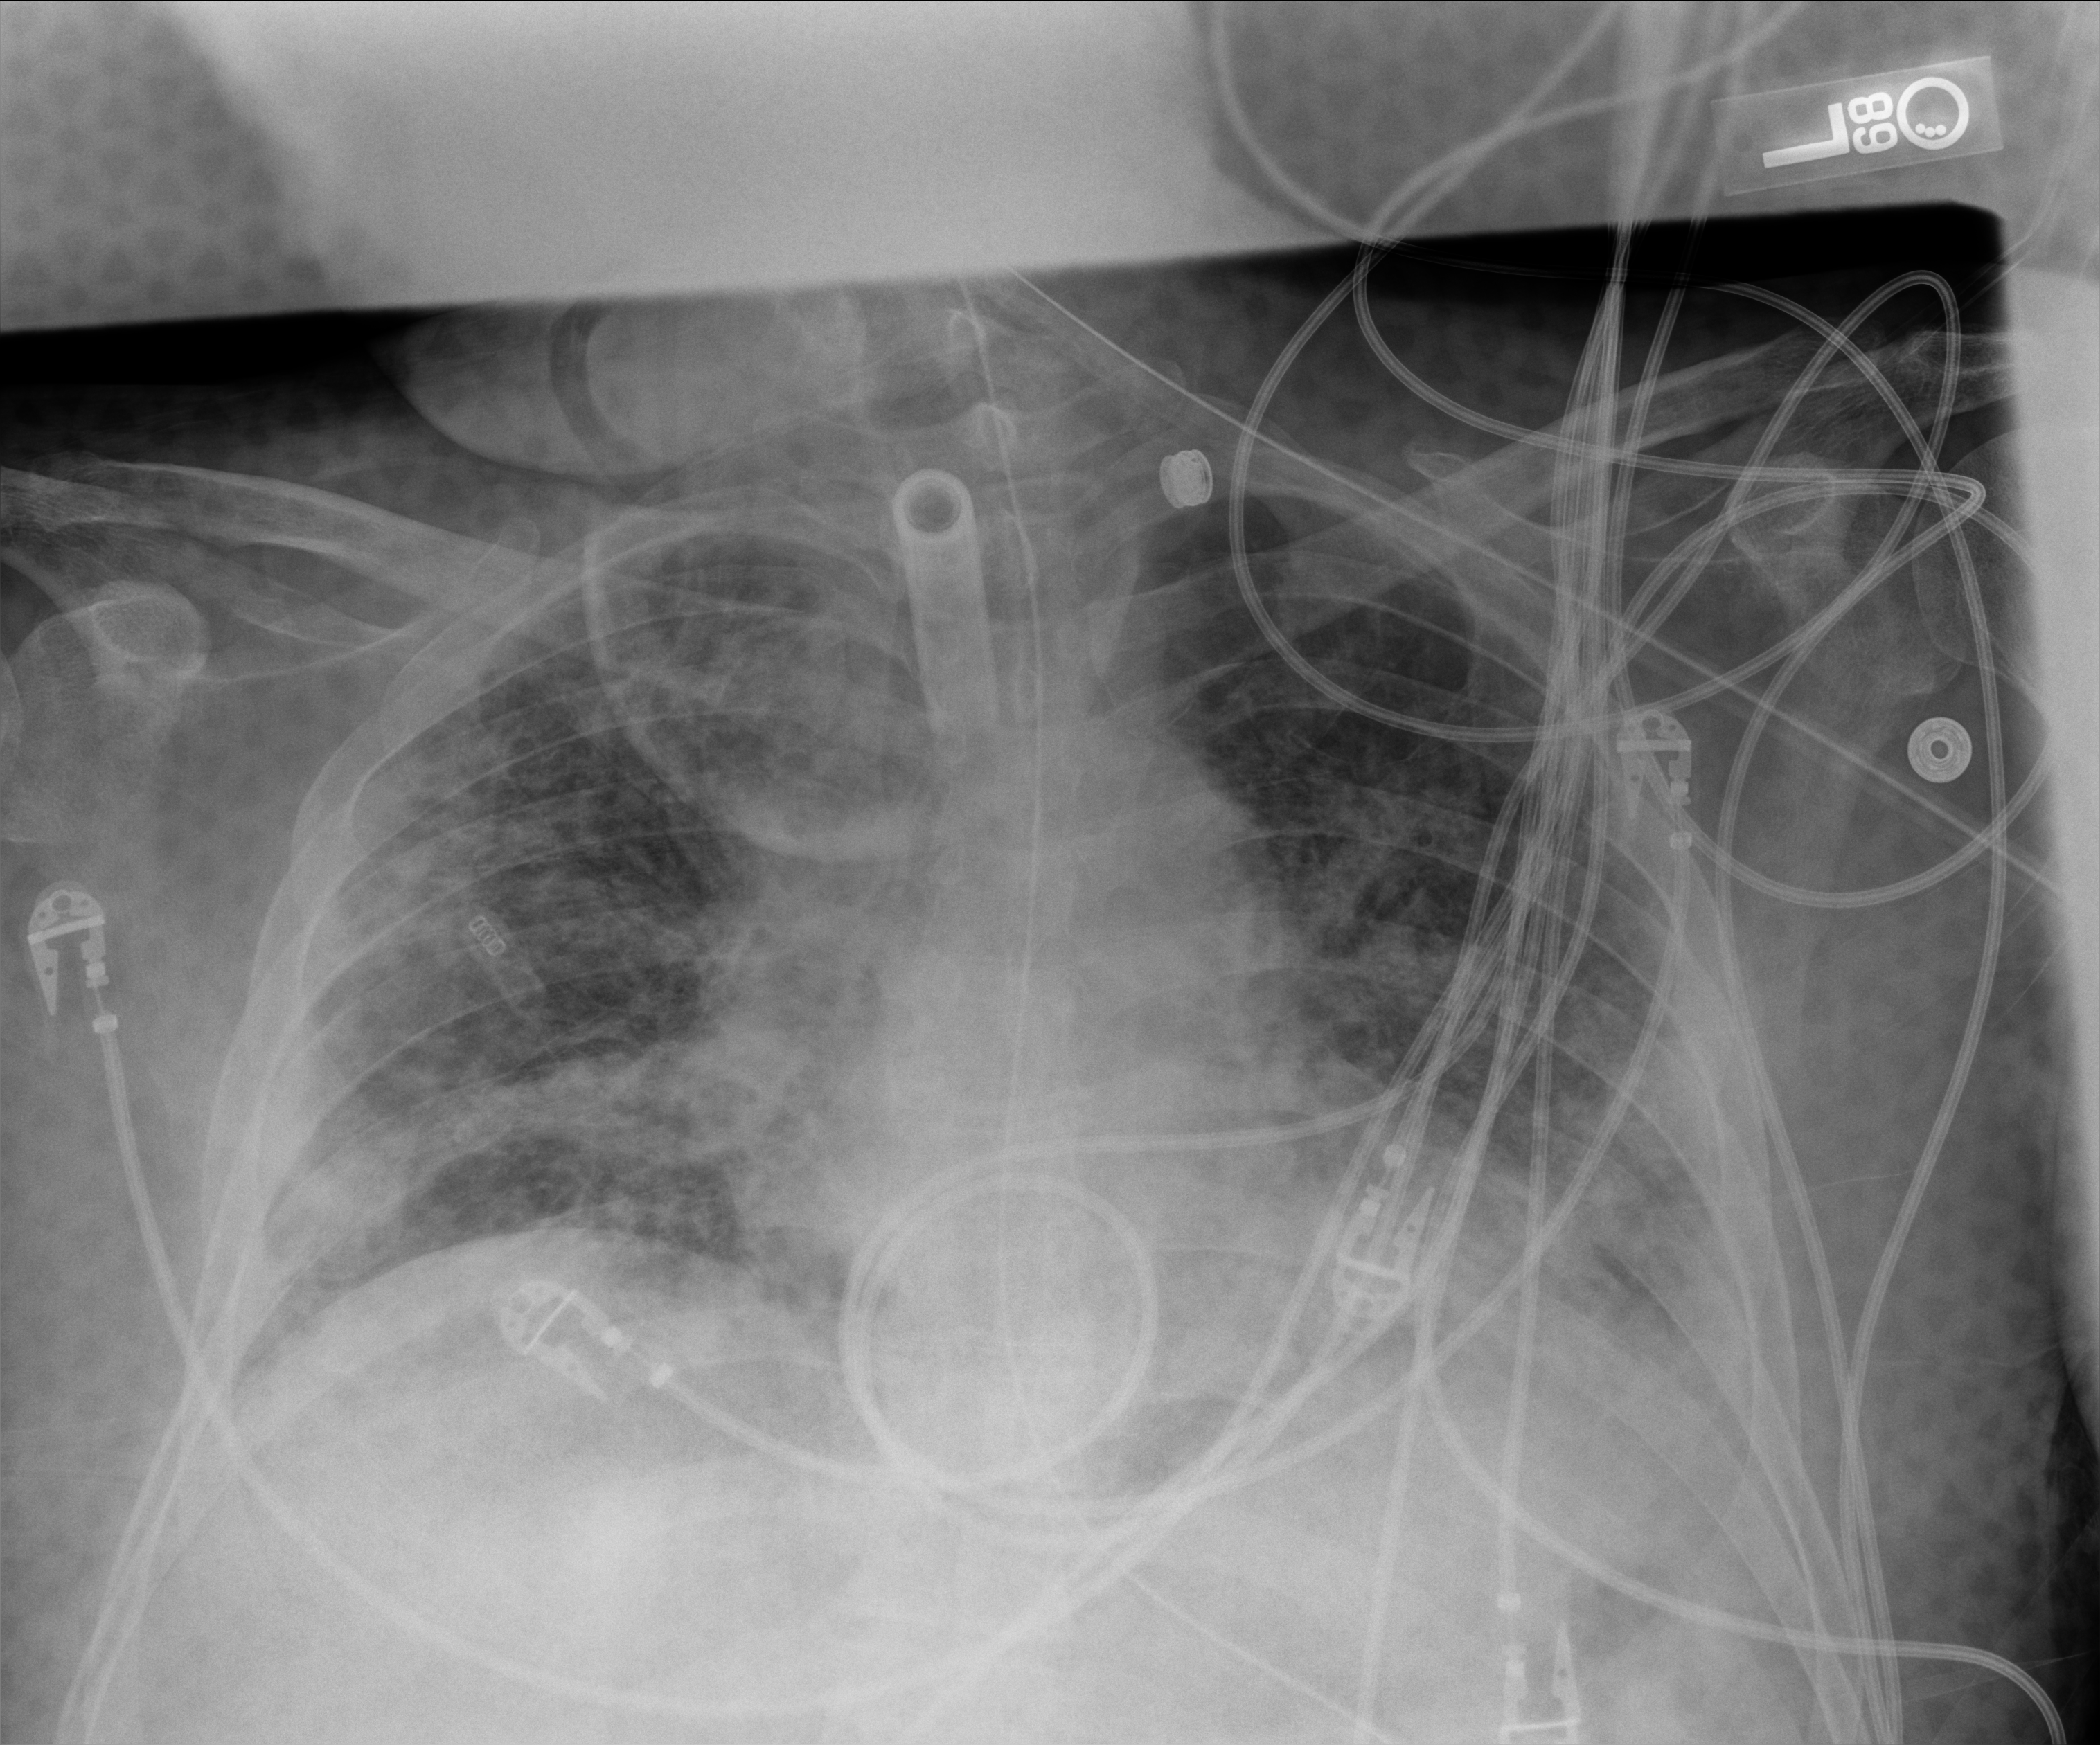
Bedside chest radiograph (digital radiography), anteroposterior (AP) projection. Patient hospitalised with COVID-19; male, aged 18–59 years.
From the hospital-stay record, not from the radiograph (when in the stay this image was taken is not recorded): length of hospital stay: 63 days; mechanically ventilated during this hospital stay: yes.